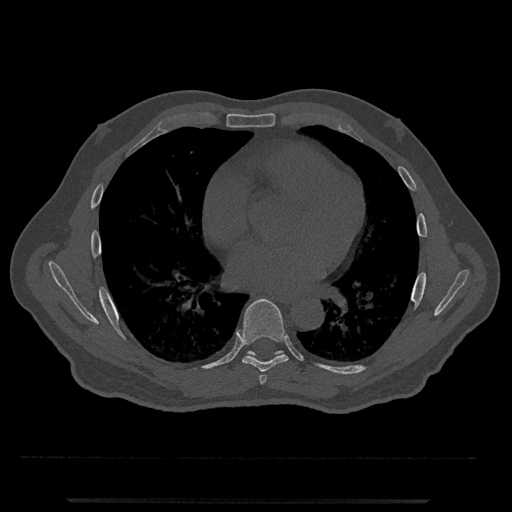
CT including the spine, one axial slice; position 674 of 797 along the scan axis; bone window (W 1800 / L 400 HU); 512 × 512 image matrix, field of view 419 × 419 mm. Male patient, age 63 years. From the clinical record (not read from this slice): primary cancer: prostate.
Outlined on this slice (semi-automatically segmented with operator editing):
- T6 vertebra: box from (x=259, y=375) to (x=267, y=384) px
- T7 vertebra: (x=236, y=298)–(x=289, y=372)
- T8 vertebra: (x=247, y=350)–(x=283, y=356)